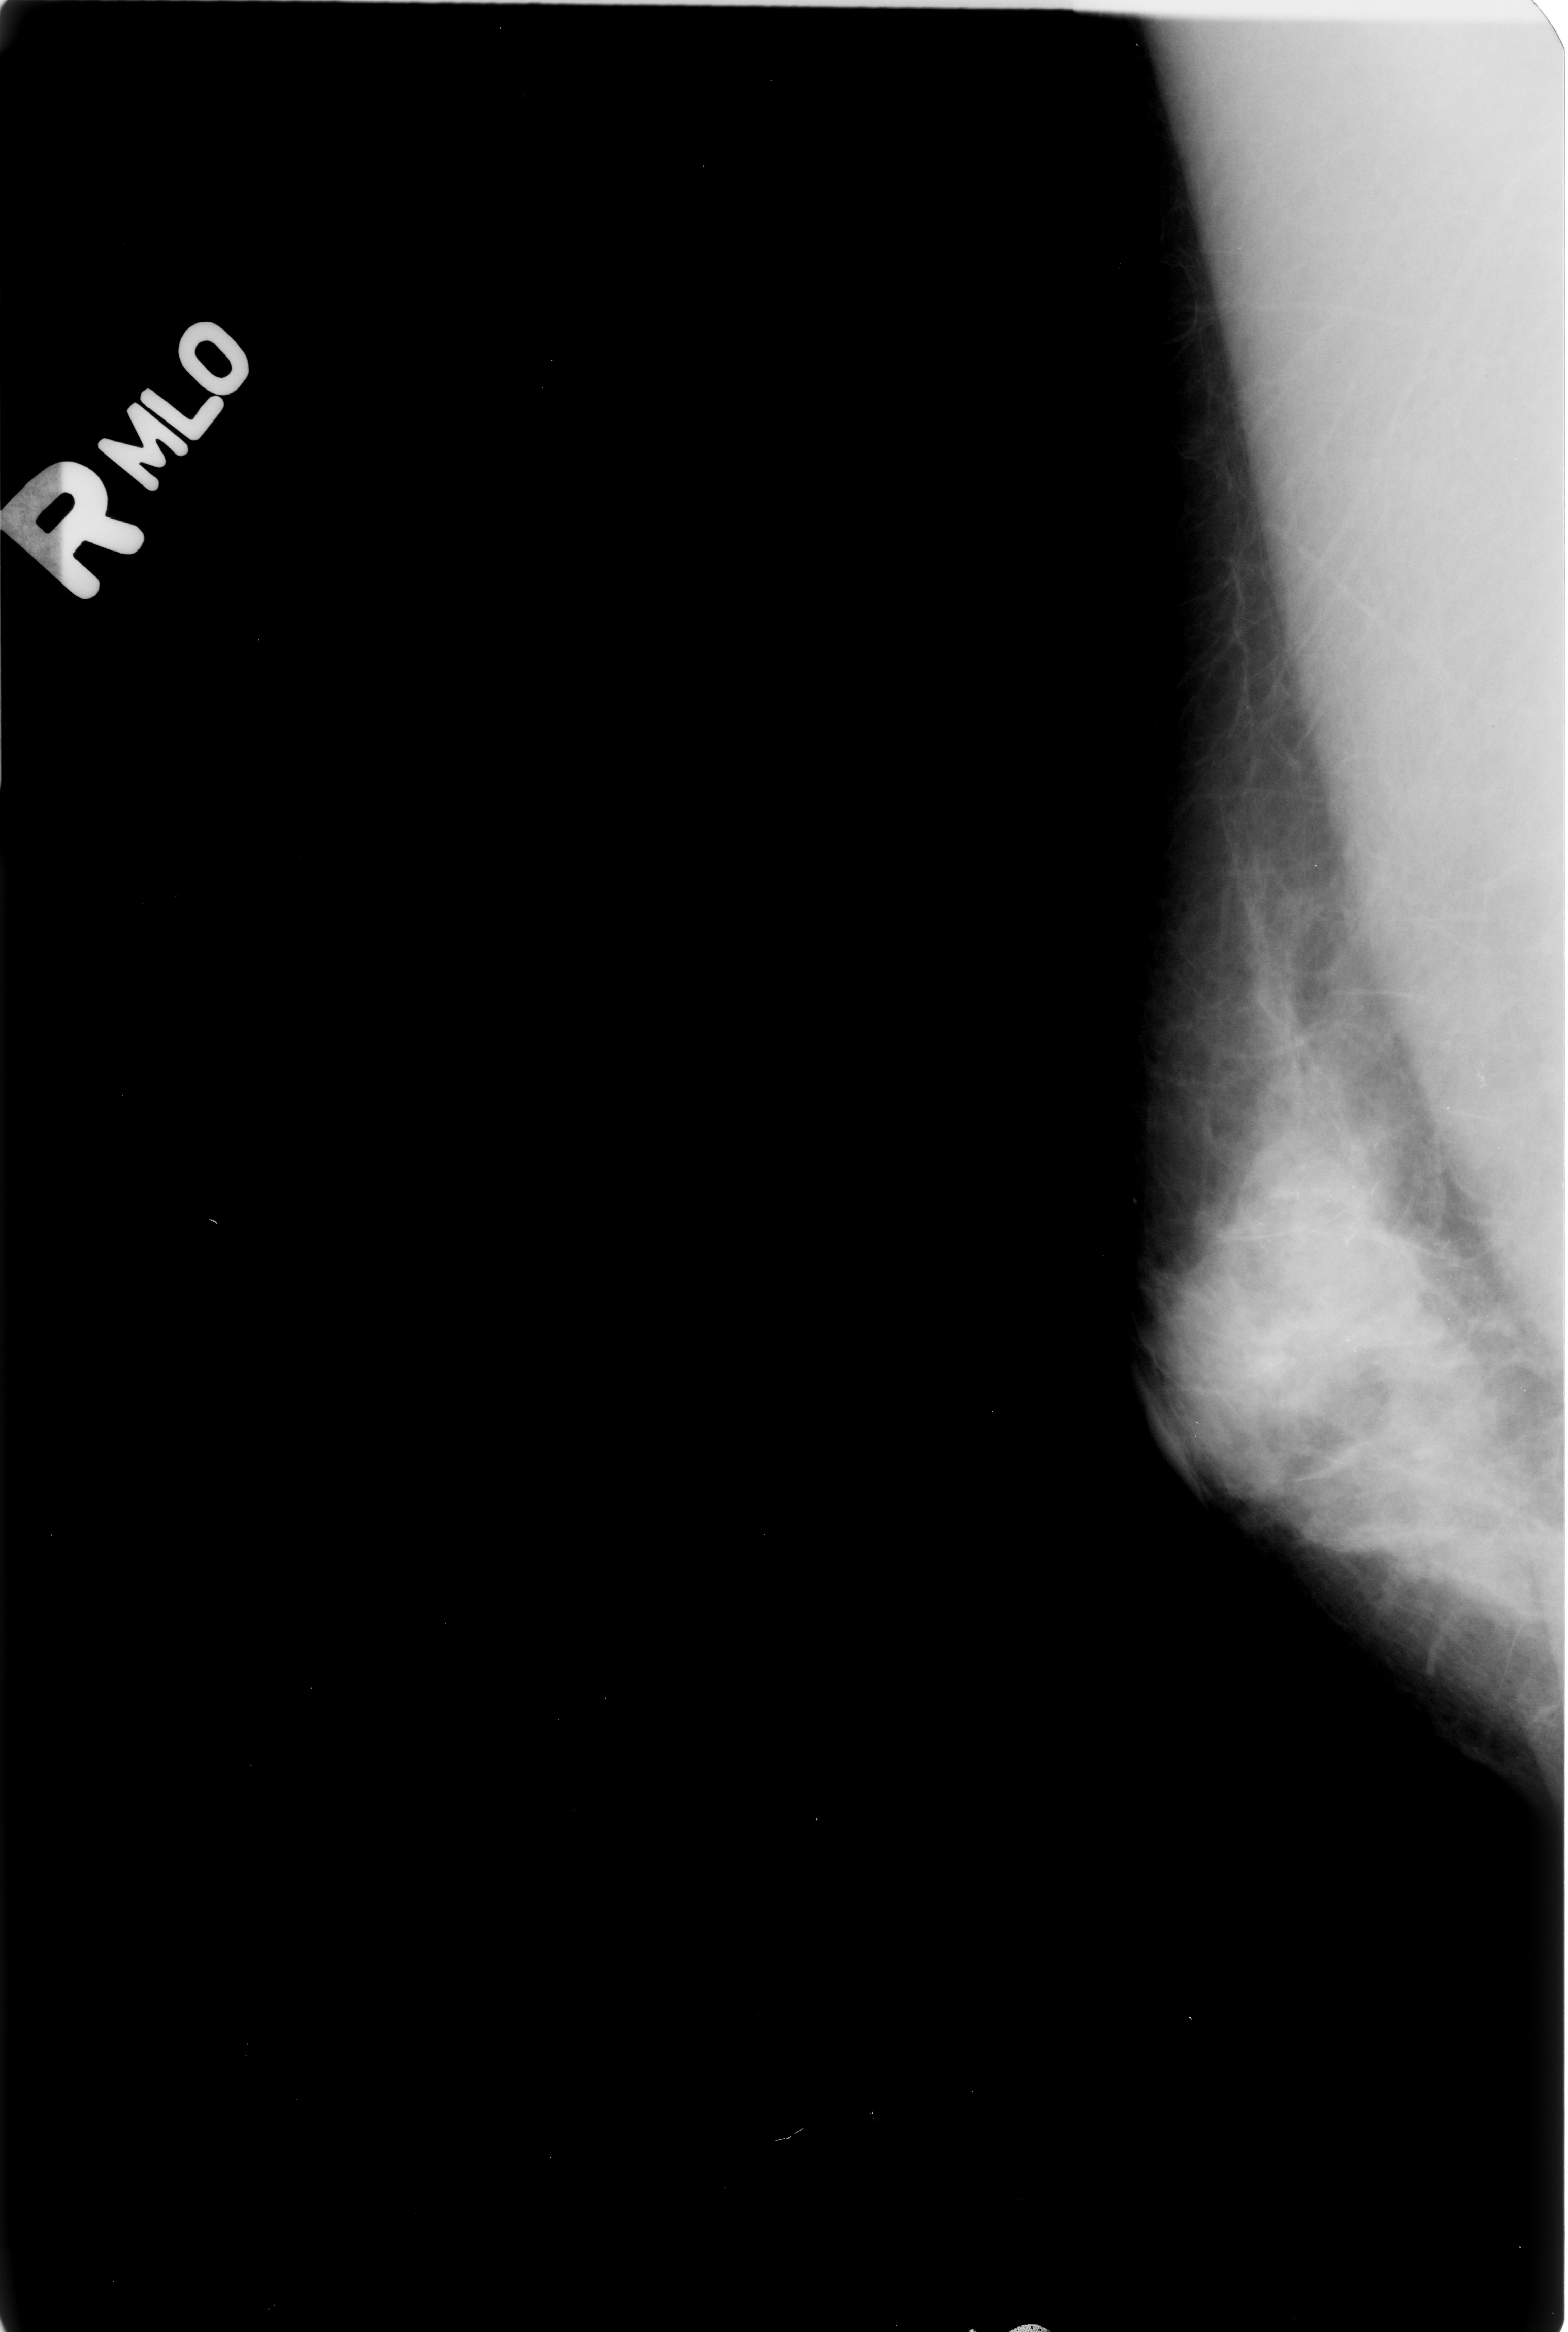
Digitized screen-film mammogram. Right breast. Mediolateral oblique (MLO) view. BI-RADS breast density category 3 (scale 1–4). 1568 × 2332 image matrix.
Expert-marked regions of interest on this film, with their recorded descriptors:
- calcifications, morphology fine linear branching, distribution segmental; BI-RADS assessment category 5; subtlety rating 3 on a 1 (subtle) to 5 (obvious) scale; pathology result (as recorded, not read from the image): malignant: bounding box (x1, y1, x2, y2) in pixels: (1190, 1035, 1532, 1427)